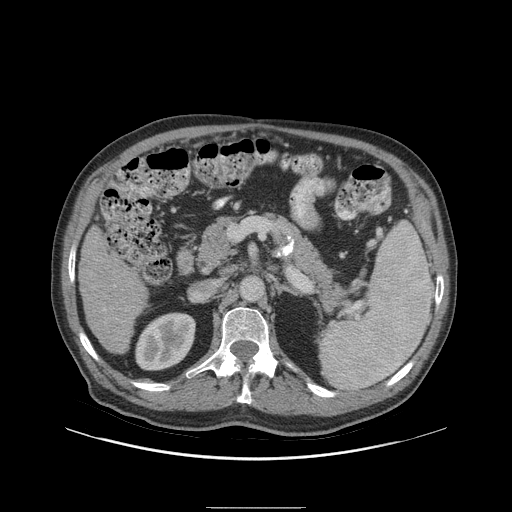
Contrast-enhanced abdominal CT (liver protocol), one axial slice; position 40 of 105 along the scan axis; reconstruction kernel STANDARD; 140 kVp; soft-tissue window (W 400 / L 40 HU); 512 × 512 image matrix, field of view 440 × 440 mm. From the clinical record (not read from this slice): diagnosis: hepatocellular carcinoma (patient treated with transarterial chemoembolisation; whether this scan precedes or follows treatment is not stated here); TNM stage (as recorded): Stage-I; Child-Pugh class: A; tumour nodularity: uninodular; tumour size: 5.1 cm.
Outlined on this slice (semi-automatic segmentation, software-assisted and operator-edited):
- liver parenchyma outside the tumour (the mass and vessels are separate outlines, so this box may not span the whole liver): box from (x=78, y=226) to (x=148, y=354) px